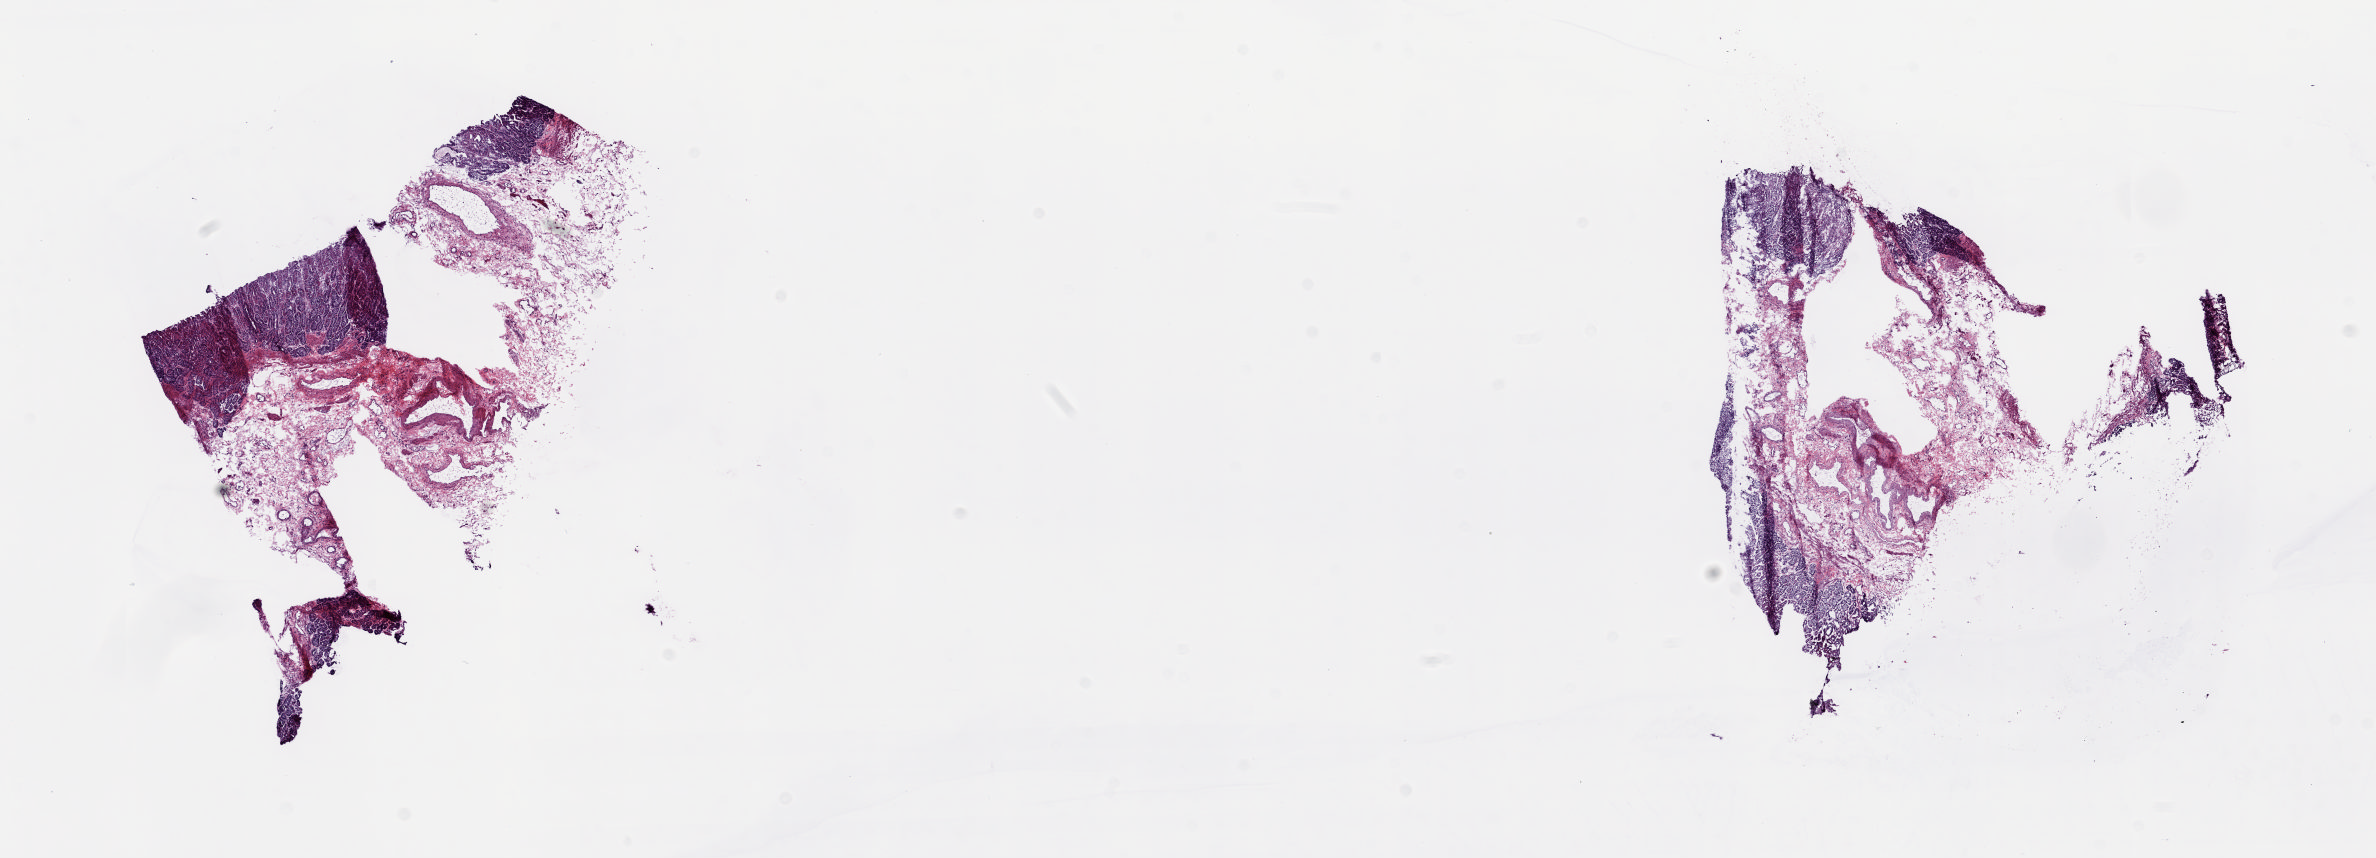
H&E whole-slide image — shown as a low-resolution overview of the whole scanned area (about 18.8 x 6.8 mm). Frozen section. Solid tissue normal (non-tumour tissue) sample from the esophagus. Male patient. Slide review estimates, as recorded: tumour cells 0%, tumour nuclei 0%, normal cells 100%, stromal cells 0%, necrosis 0%. Infiltration values recorded for this section: lymphocyte infiltration 5%, monocyte infiltration 0%, neutrophil infiltration 0%.
* this section: solid tissue normal (non-tumour) sample from the same patient
* patient diagnosis: Adenocarcinoma, NOS (lower third of esophagus)